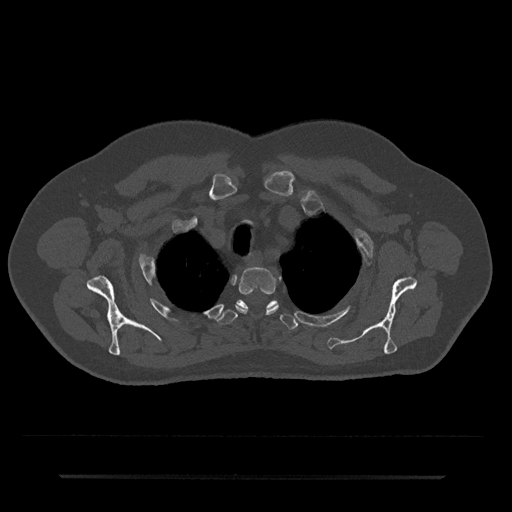
CT including the spine, one axial slice. Position 590 of 797 along the scan axis. 120 kVp. Bone window (W 1800 / L 400 HU). 0.5 mm slice thickness. 512 × 512 image matrix. Patient: male, 69 years. Case-level facts recorded for this patient, not image findings: primary cancer: prostate.
Annotated regions visible in this slice (semi-automatic segmentation, software-assisted and operator-edited):
- T2 vertebra: box from (x=235, y=267) to (x=279, y=314) px
- T3 vertebra: (x=217, y=299)–(x=297, y=330)